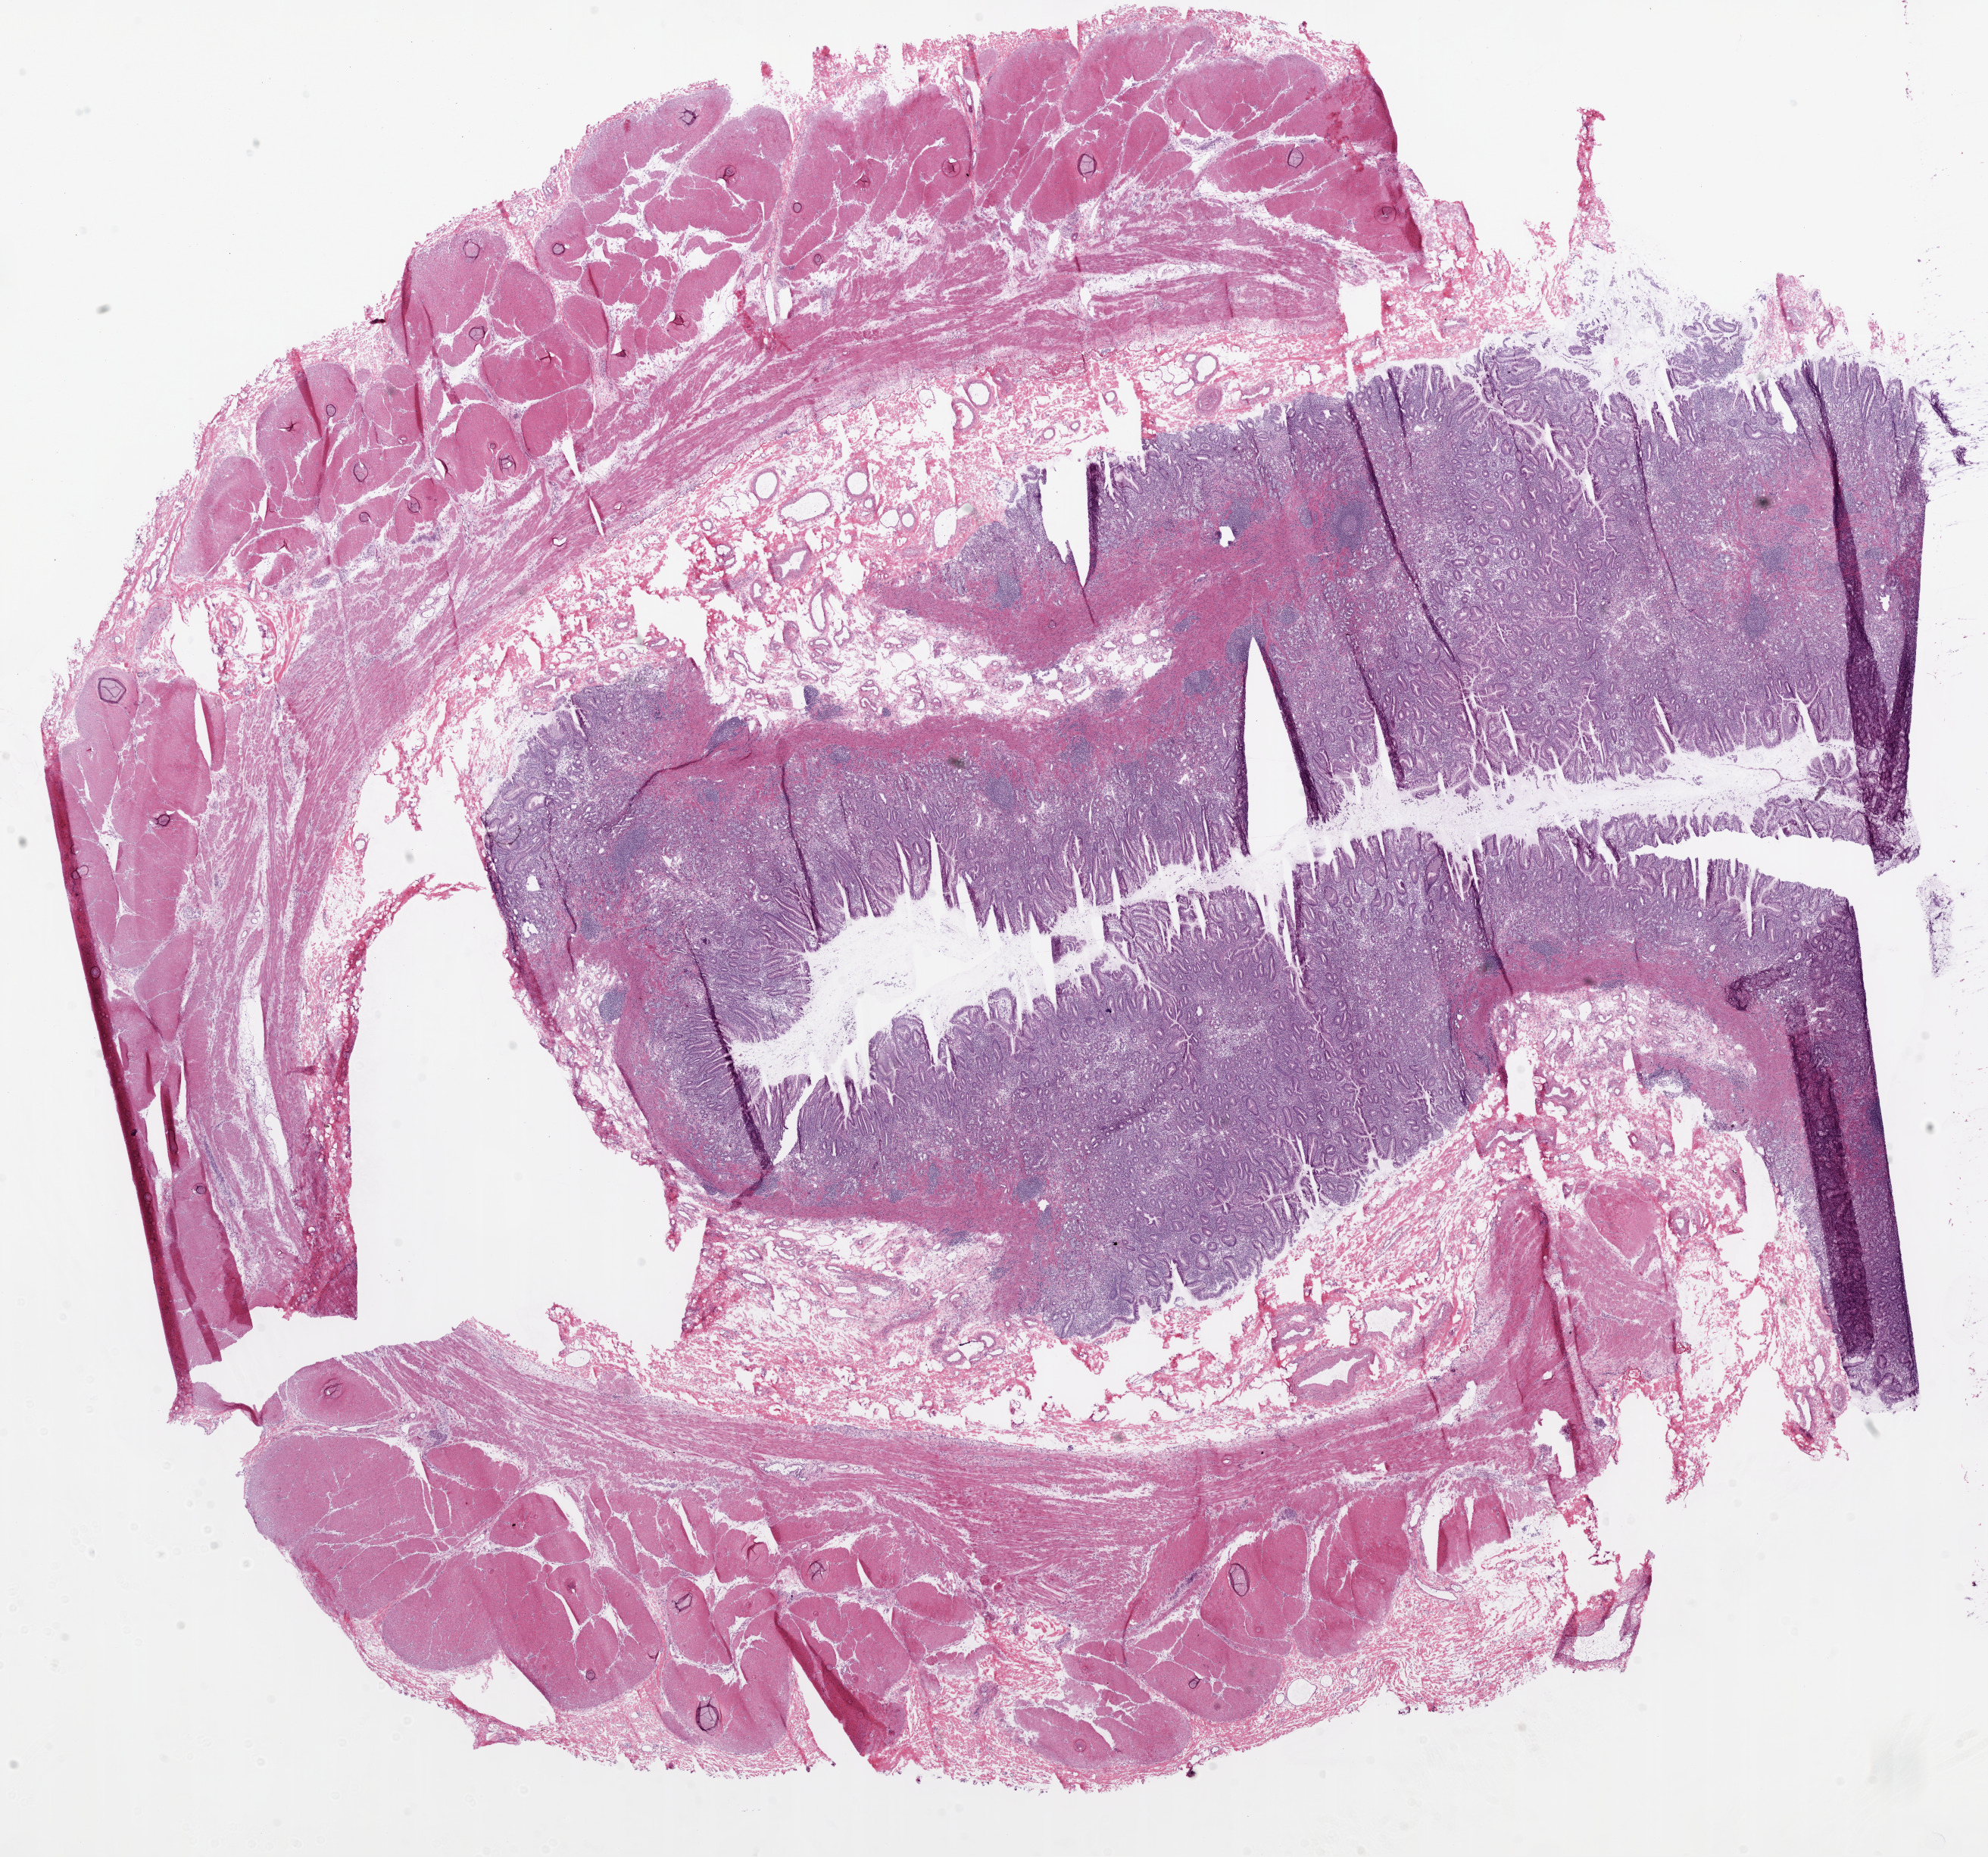
Digitized H&E tissue section (whole slide), shown as a low-resolution overview of the whole scanned area (about 21.1 x 19.7 mm); frozen section from the top of the tissue portion; sample: solid tissue normal (non-tumour tissue), stomach. Female, age 78 years at initial diagnosis.
This section: solid tissue normal (non-tumour) sample from the same patient. Patient diagnosis: Adenocarcinoma, NOS.